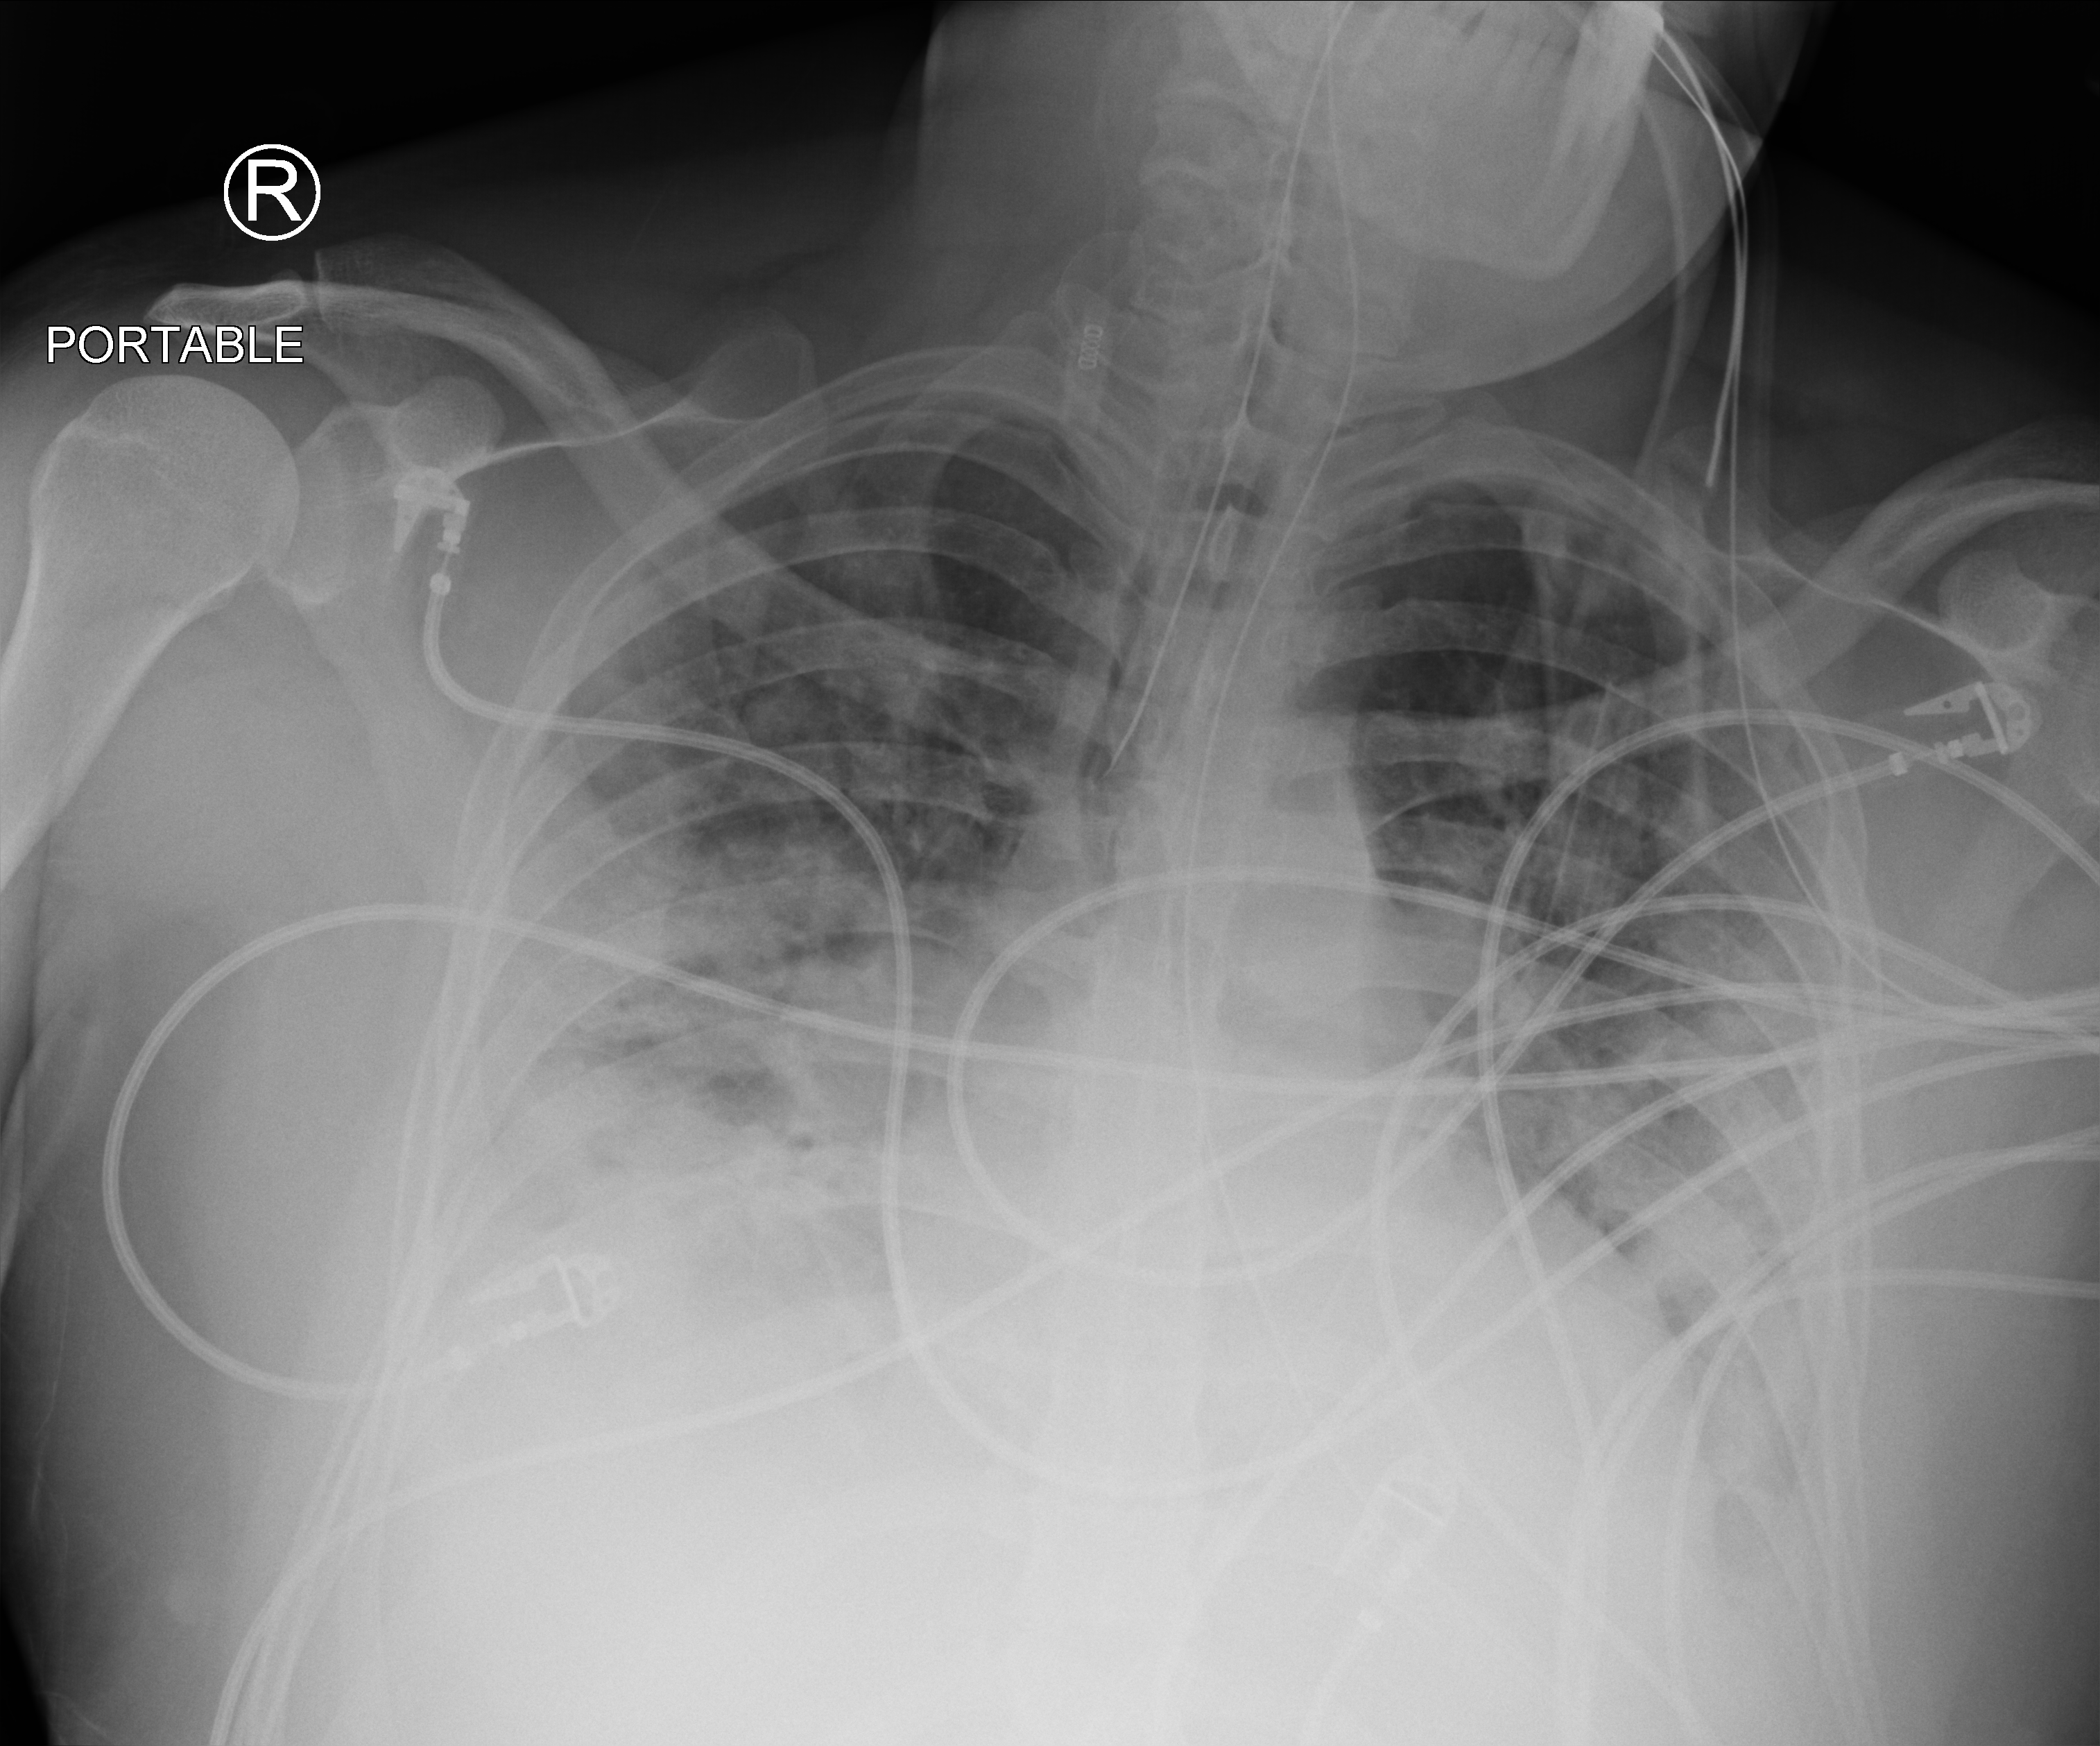
Chest X-ray (portable). Patient hospitalised with COVID-19; male, aged 18–59 years.
Admission-level facts for this patient (not findings on this image; timing relative to this image not recorded): mechanically ventilated during this hospital stay: yes; length of hospital stay: 22 days; diabetes (admission record): no.